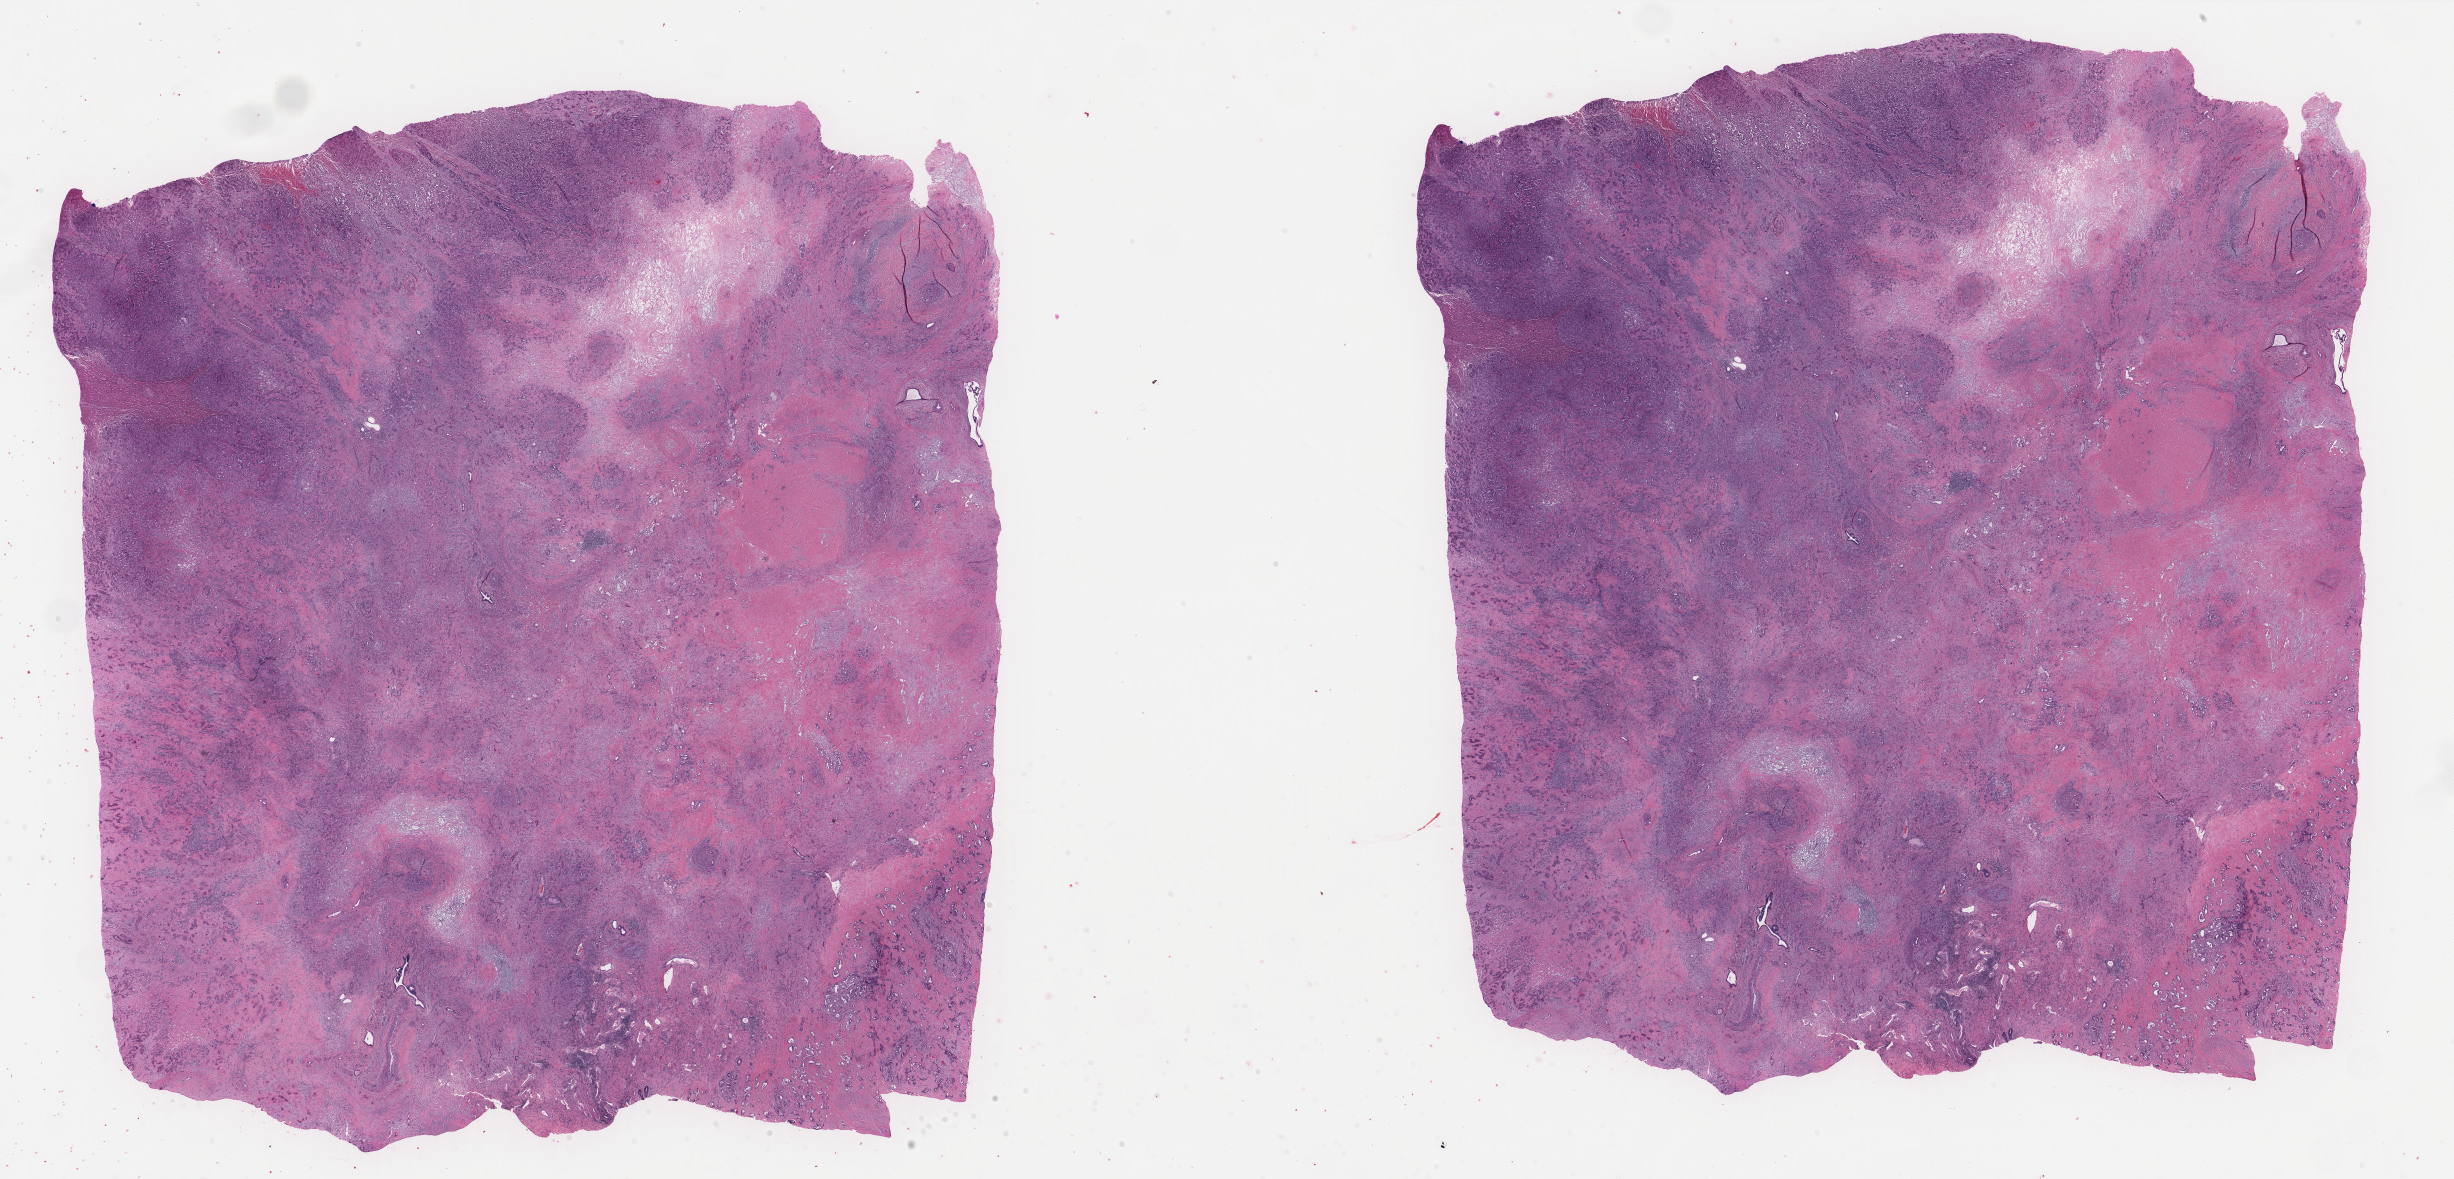
Digitized Hematoxylin and eosin (H&E) stained tissue section (whole slide), shown as a low-resolution overview of the whole scanned area (about 38.8 x 18.7 mm, from a 40x scan). Formalin-fixed paraffin-embedded (FFPE) diagnostic section. Primary tumour sample from the bile duct. Patient: female, age at initial diagnosis 61 years.
Diagnosis: Cholangiocarcinoma (intrahepatic bile duct).